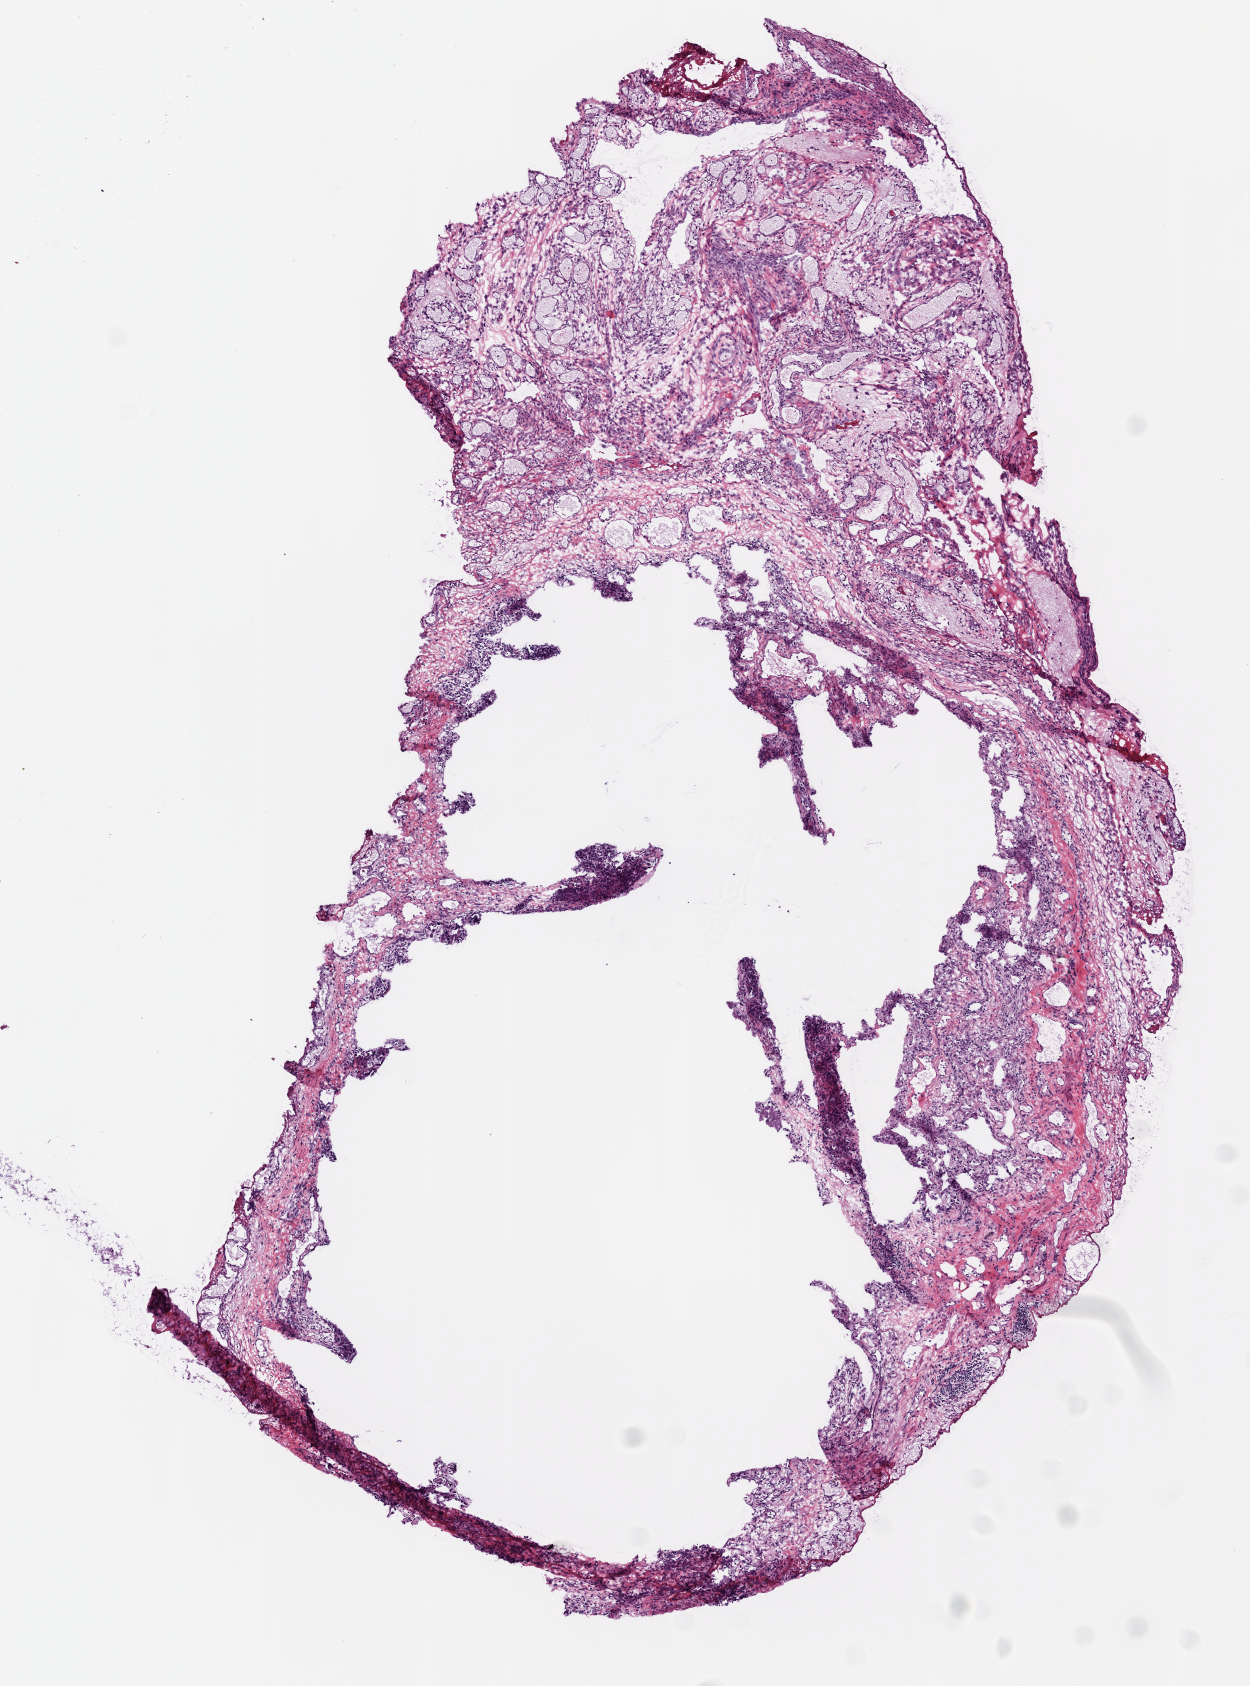
Whole-slide histology image, H&E — a low-resolution overview of the entire scanned area, about 5.0 x 6.8 mm; frozen section from the top of the tissue portion; sample: solid tissue normal (non-tumour tissue), lung. Patient: male, age at initial diagnosis 68 years.
This section: solid tissue normal (non-tumour) sample from the same patient. Patient diagnosis: Squamous cell carcinoma, NOS.